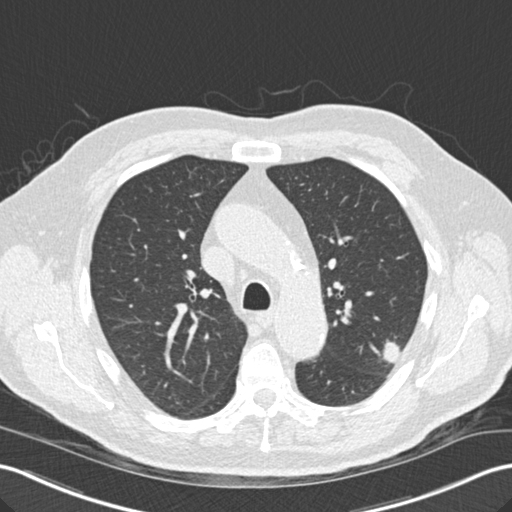
Low-dose screening chest CT, one axial slice. Position 105 of 157 along the scan axis. Reconstruction kernel B30f. Lung window (W 1500 / L -600 HU). 2 mm slice thickness. 512 × 512 image matrix, field of view 354 × 354 mm.
Structures marked on this image (manually delineated by an expert):
- lesion 1 (tumor, upper lobe of left lung): box from (x=383, y=342) to (x=401, y=363) px